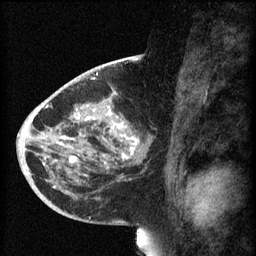
Breast MRI (dynamic contrast-enhanced), one sagittal slice. Position 31 of 60 along the scan axis. 3 images stored at this slice position (order not interpretable as contrast timing). 1.5 T. TE 4.2 ms, TR 8.1 ms. 2 mm slice thickness. 256 × 256 image matrix. Female patient, age 44 years.
Outlined on this slice (semi-automatically segmented with operator editing):
- analysis volume of interest (the breast-tissue region the enhancement analysis was run in; not a lesion): bounding box [x1, y1, x2, y2] px = [59, 110, 151, 169]
- tumour enhancement mask (voxels above the 70 % enhancement threshold inside the analysis volume of interest): [60, 110, 139, 169]